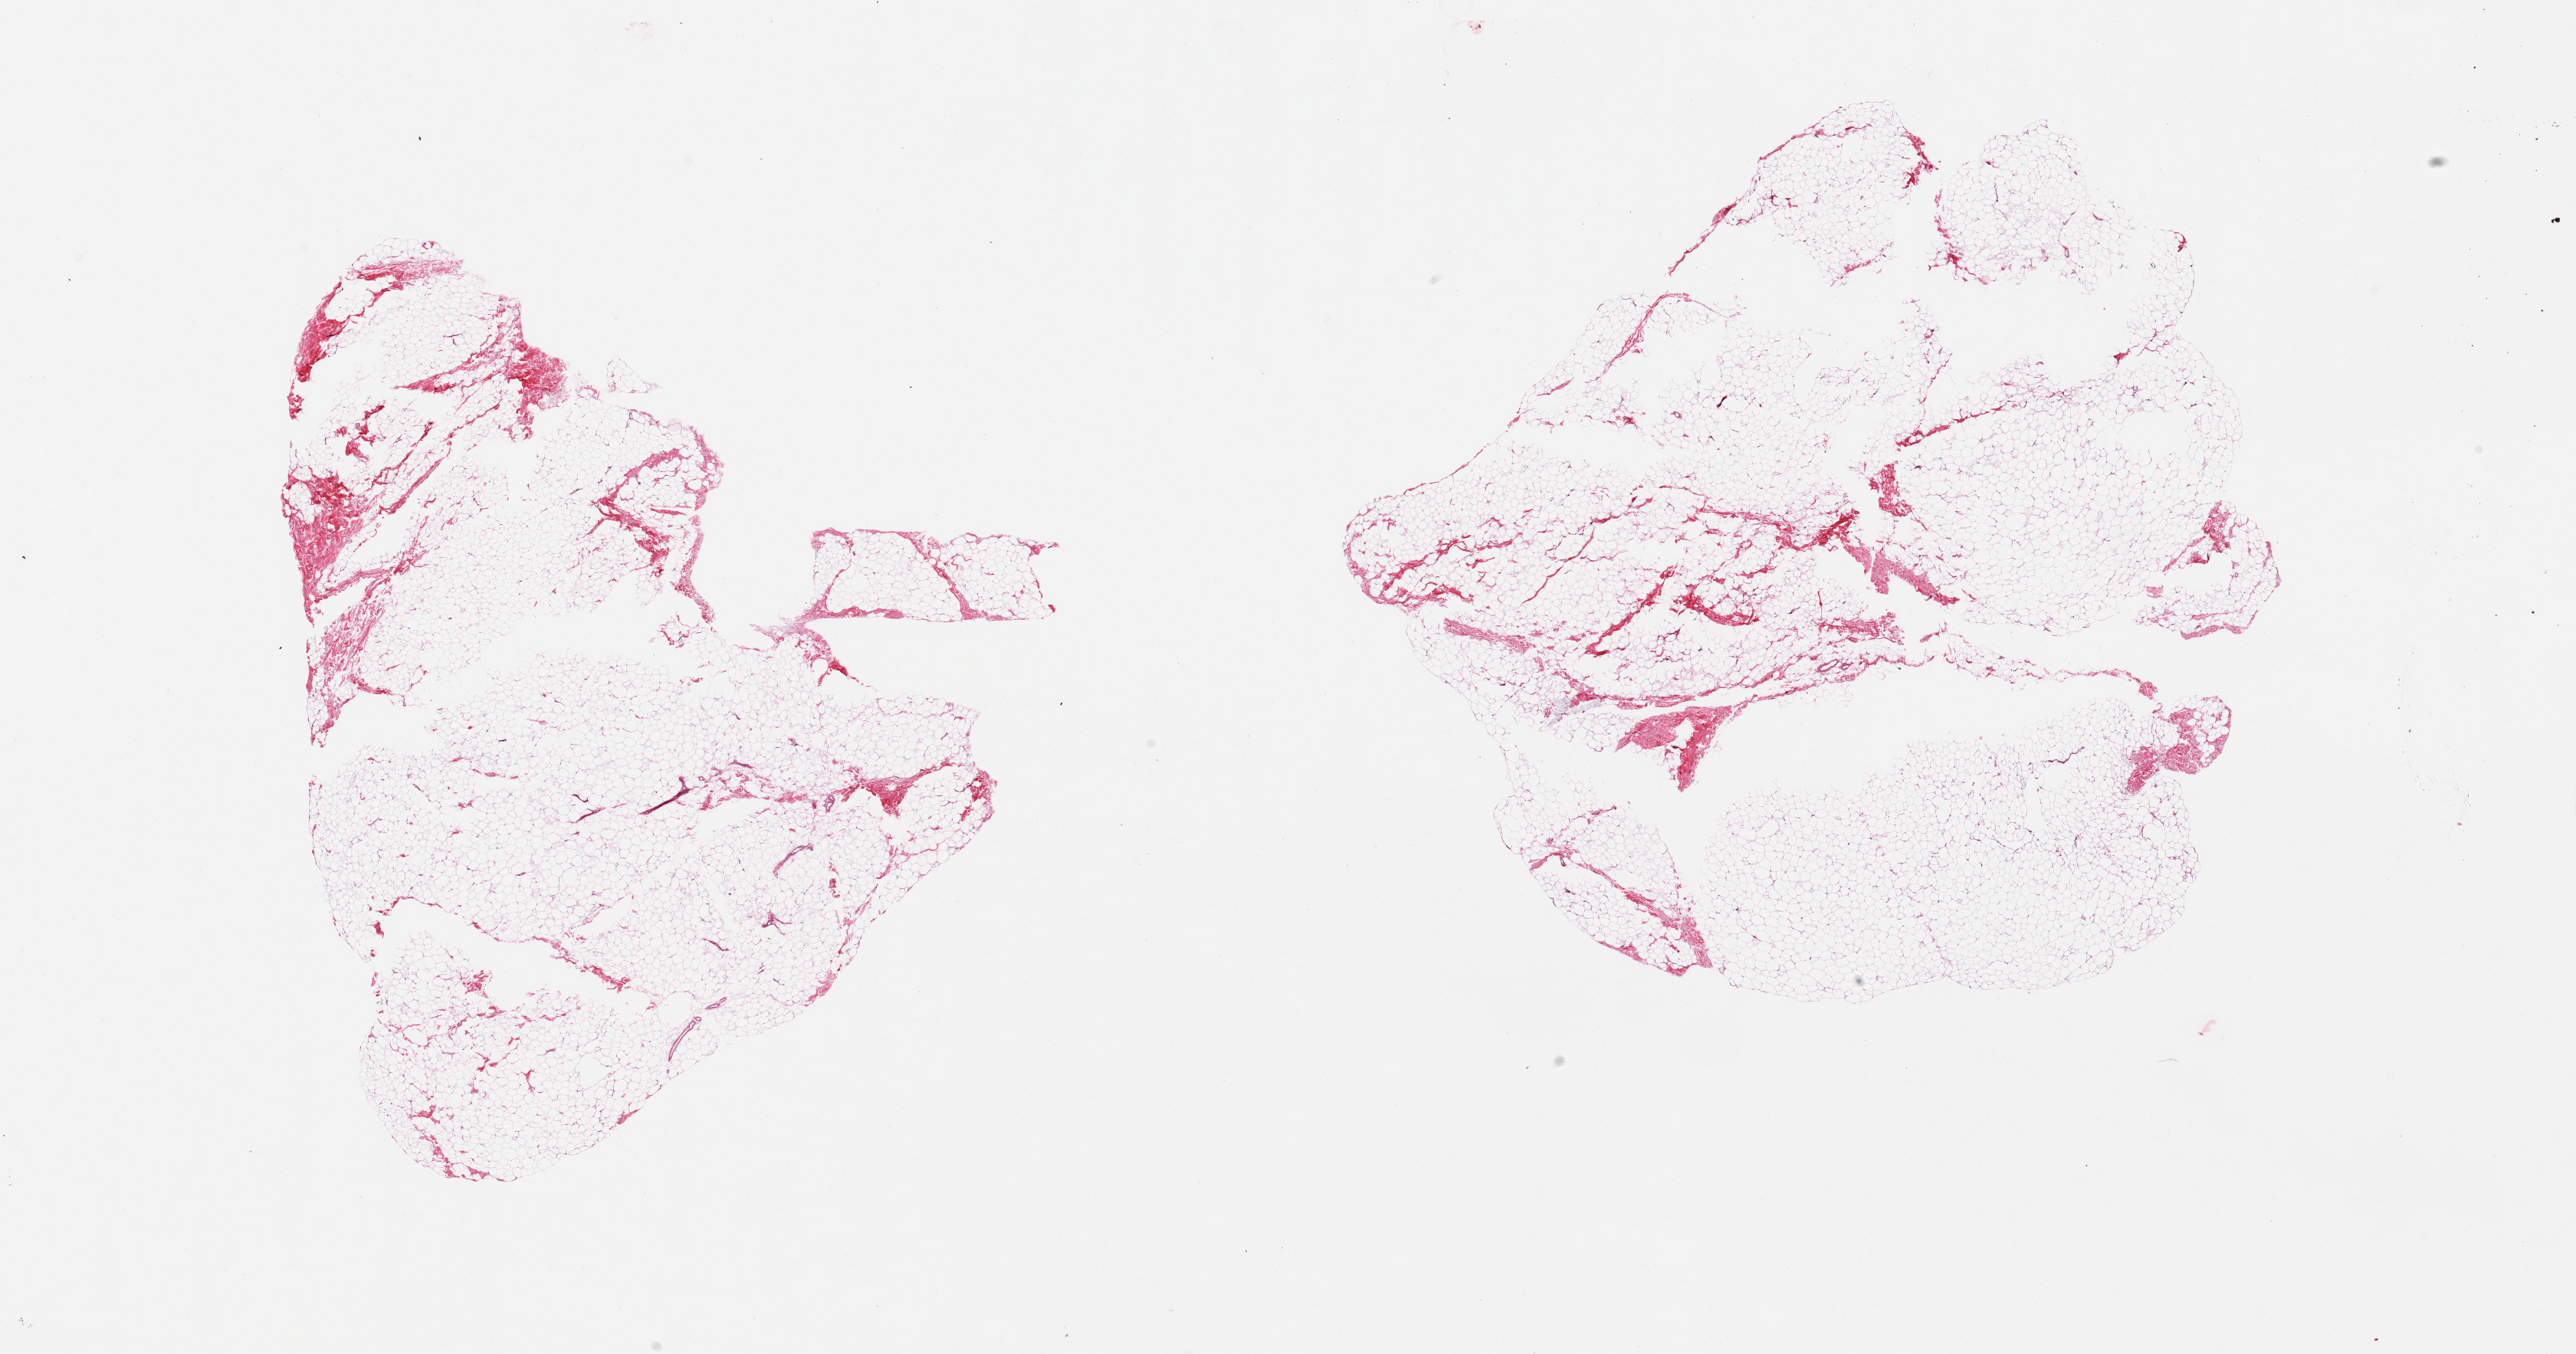
Digitized H&E-stained section, low-resolution overview of the scanned area, about 26.6 x 14.0 mm. PAXgene-fixed paraffin-embedded (PFPE) section. Sampled site (target tissue): breast. Donor tissue sample.
Pathologist's review note for this sample: 2 pieces, fibroadipose tissues only, no ductal elements.